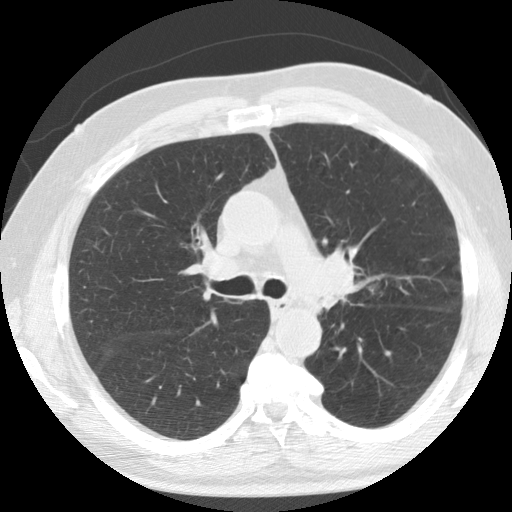
Axial slice from a low-dose chest CT screening exam, second annual screen, lung window (W 1500 / L -600 HU), standard (soft-tissue) reconstruction kernel (STANDARD), slice 49 of 133 in the series, 512 × 512 image matrix, field of view 342 × 342 mm. Male participant, aged 74 years at enrolment. Current smoker at enrolment.
Expert reader's lesion annotation, bounding box <301,242,367,310> (left, top, right, bottom; pixels). No non-calcified nodule or mass ≥4 mm was recorded by the screening reader at this exam. Official screen result: positive, other. Later outcome: lung cancer diagnosed 274 days after this screen — non-small cell carcinoma, left upper lobe, poorly differentiated (G3), stage IIB (AJCC 6th edition).